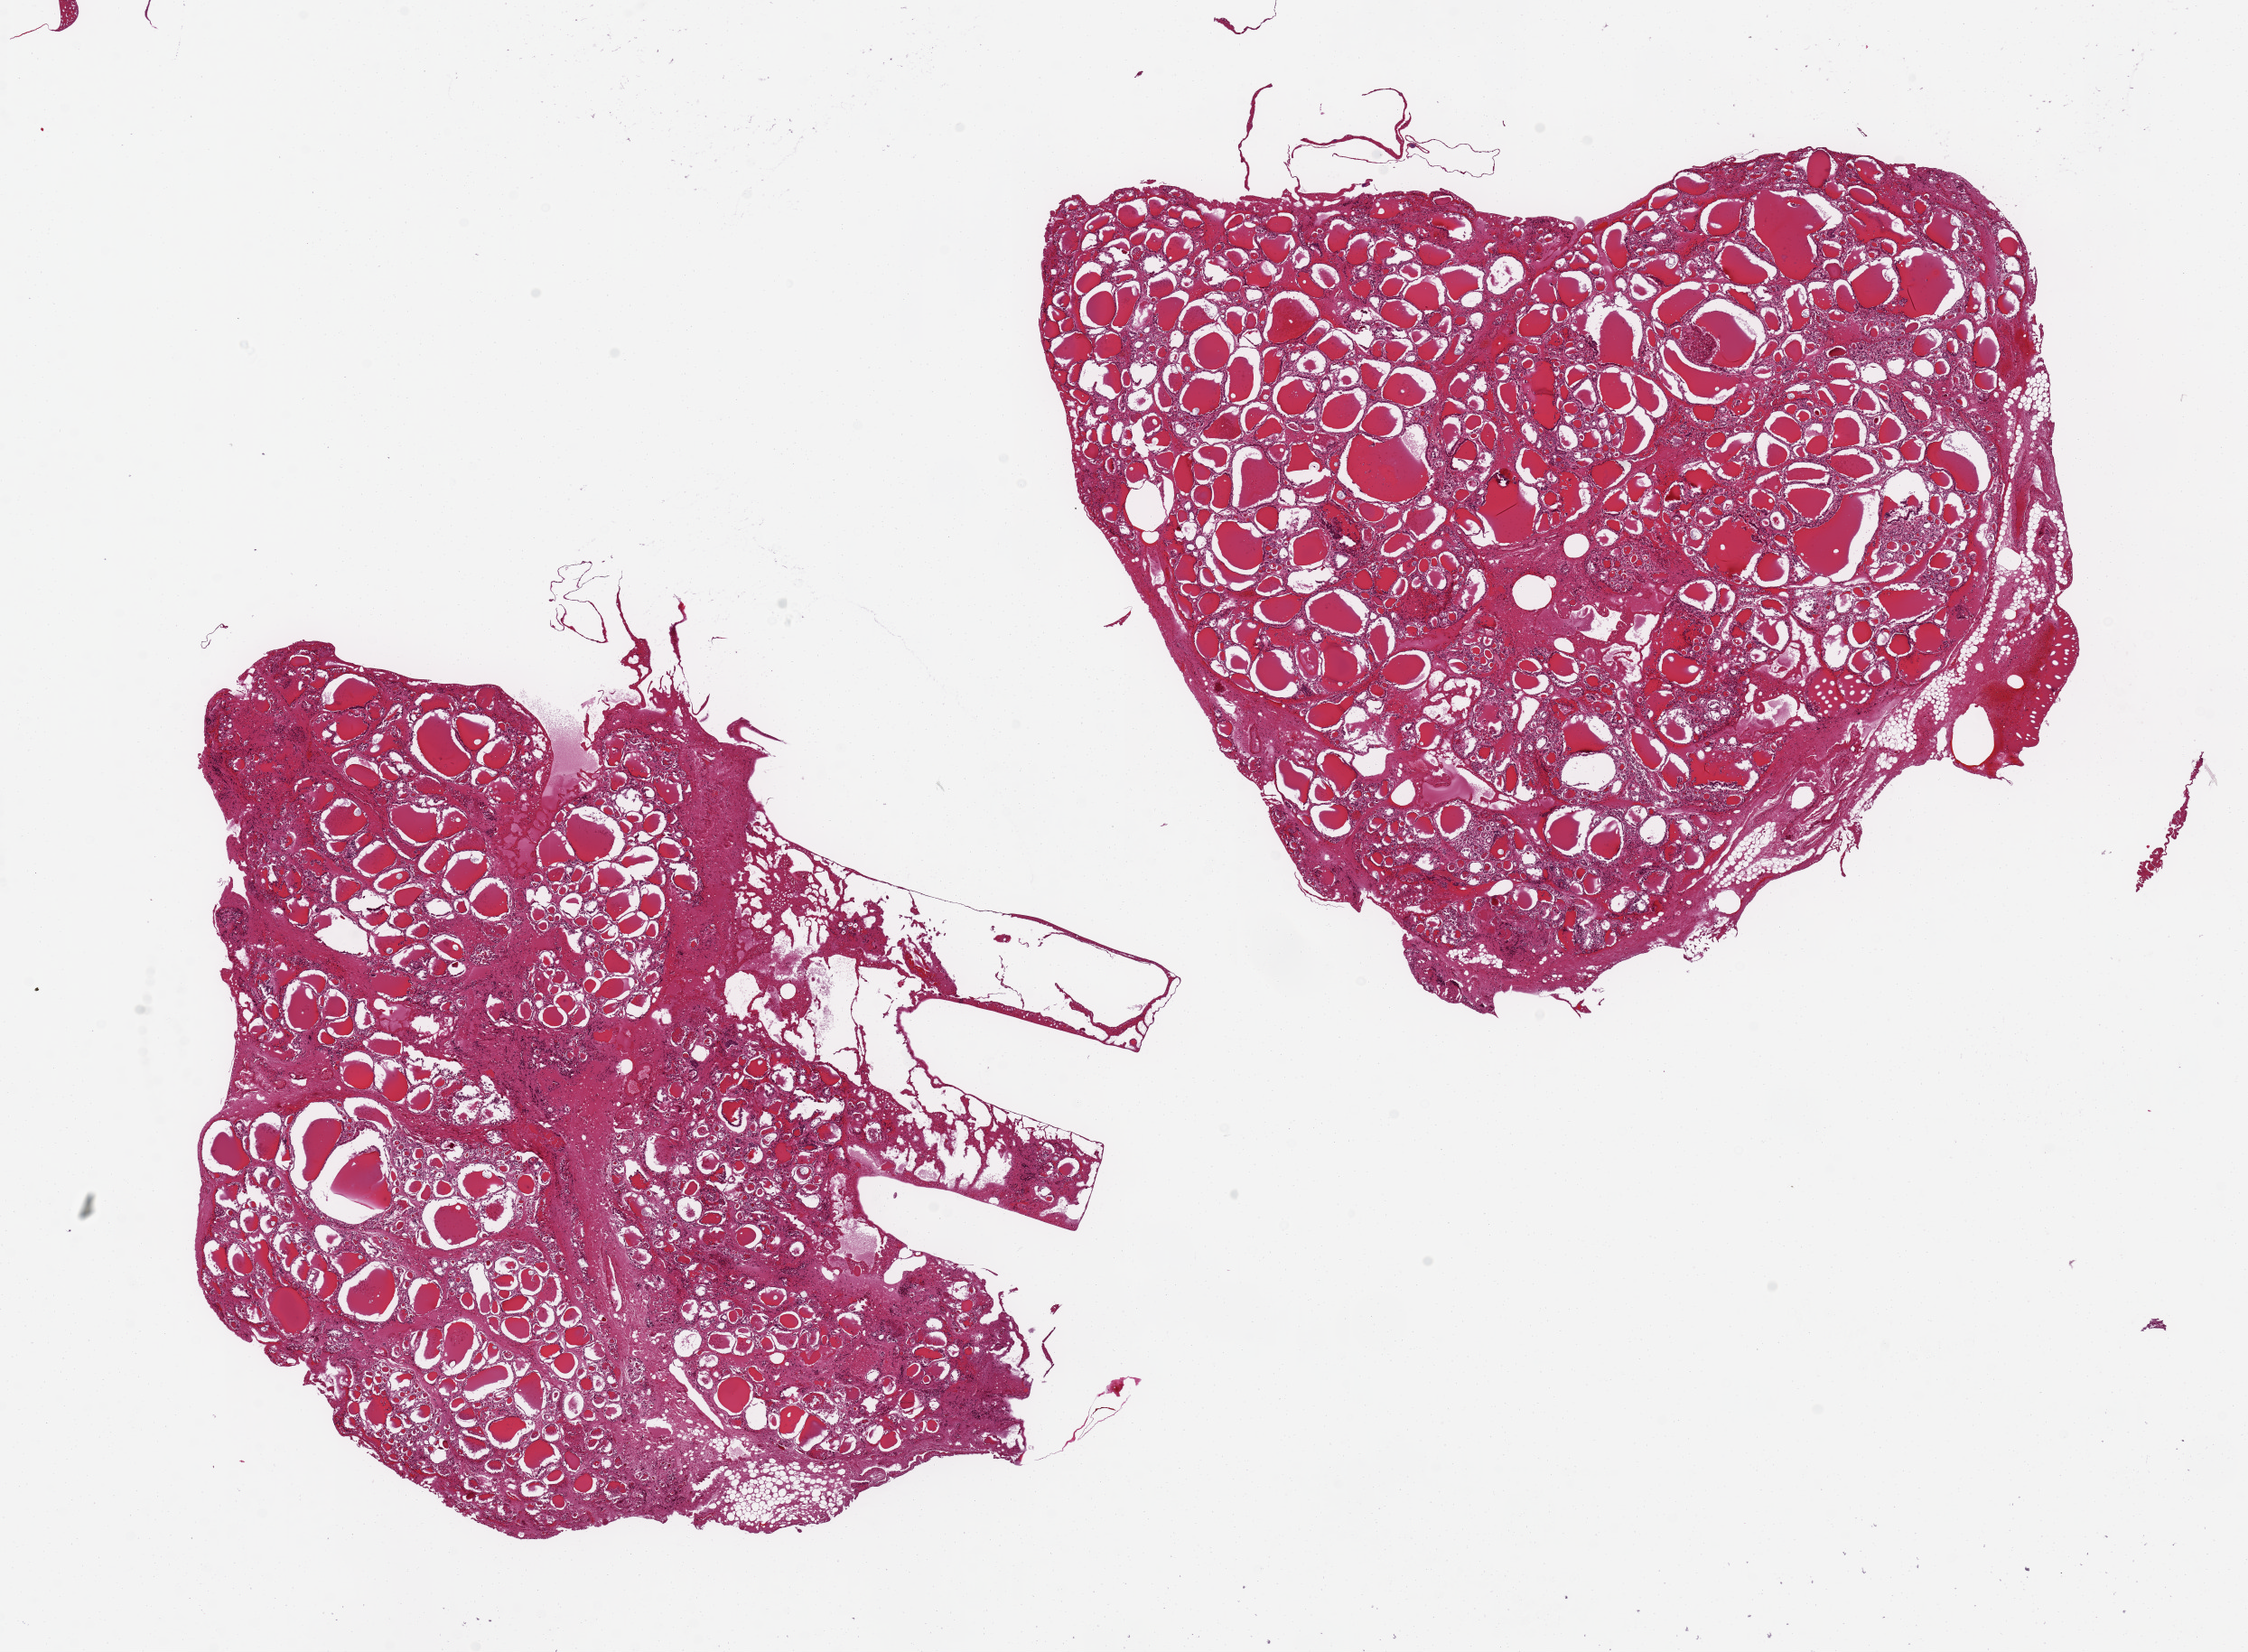
Digitized haematoxylin and eosin-stained section — a low-resolution overview of the entire scanned area, about 19.7 x 14.5 mm; PAXgene-fixed paraffin-embedded (PFPE) section; section of thyroid (target tissue); donor tissue sample. Donor: female.
Review note (as recorded): 2 pieces 7x6.7 & 8x7 mm.